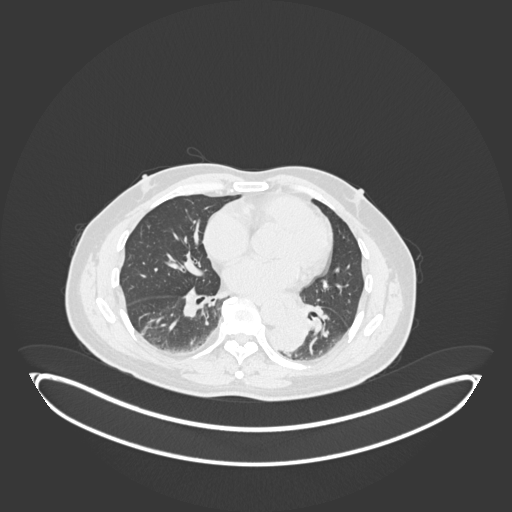
Chest CT, one axial slice. Position 81 of 258 along the scan axis. Lung window (W 1500 / L -600 HU). 1 mm slice thickness. 512 × 512 image matrix, field of view 500 × 500 mm. Male patient, age 54 years. Case-level facts recorded for this patient, not image findings: clinical TNM (as recorded): T3 N0 M0.
Outlined on this slice (bounding box drawn by a radiologist):
- lung tumour (recorded histology: squamous cell carcinoma): bounding box (x1, y1, x2, y2) in pixels: (268, 309, 312, 358)